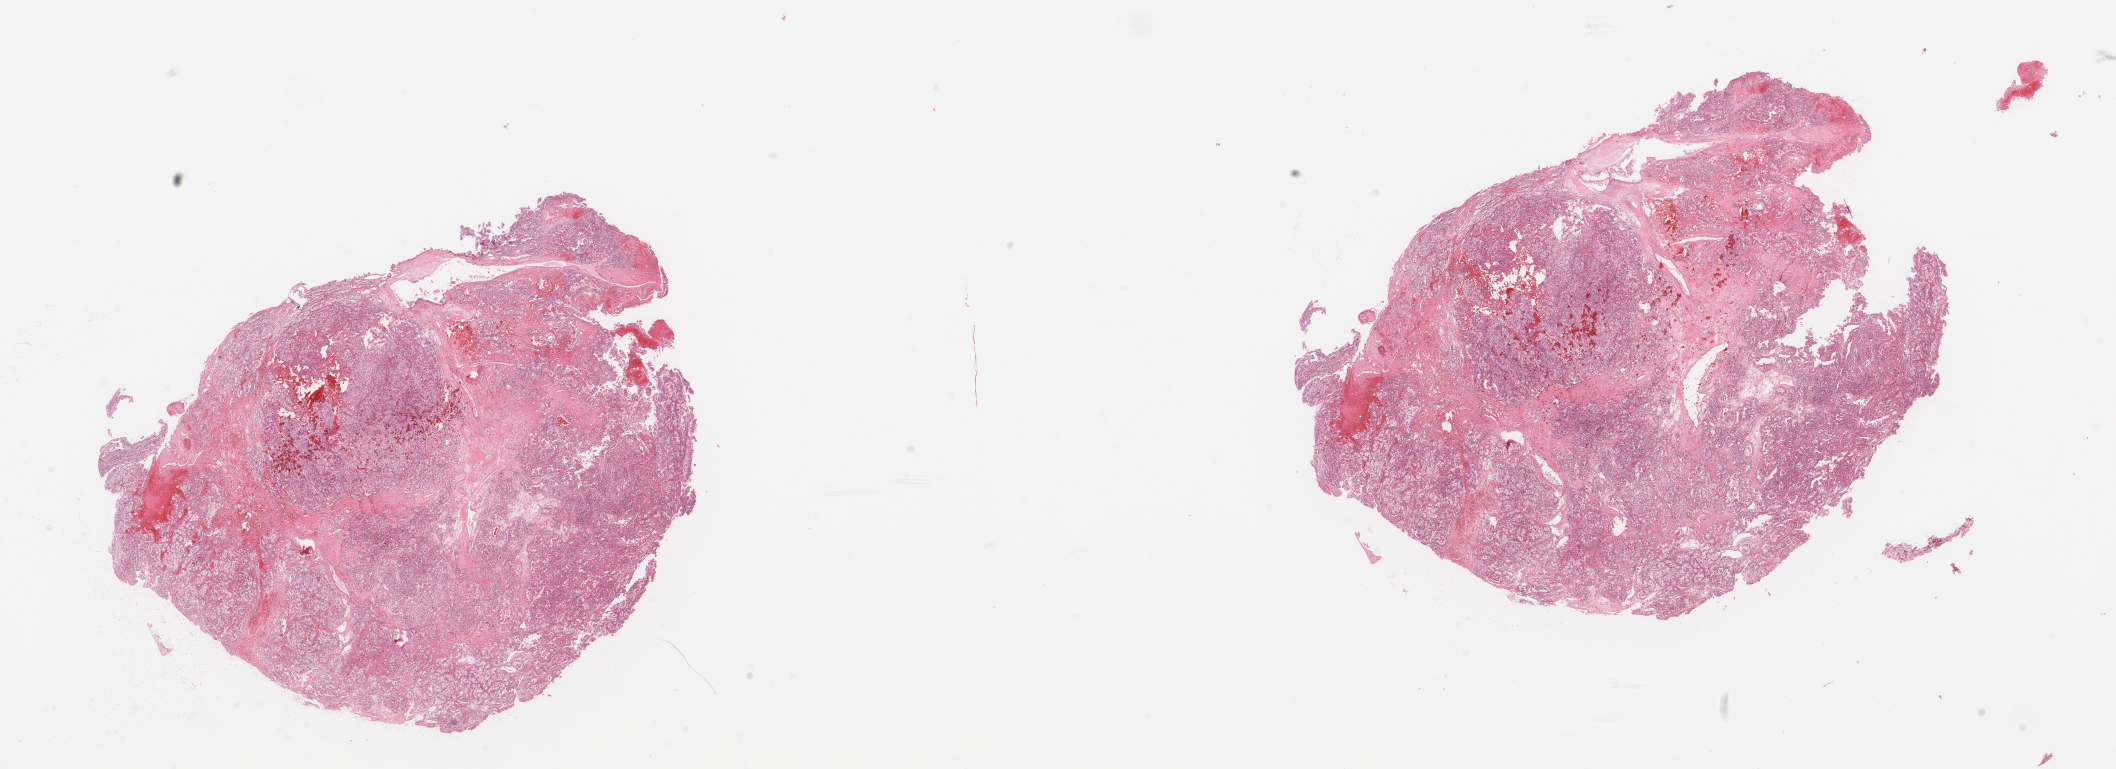
Hematoxylin and eosin (H&E) stained whole-slide image — whole scanned area (about 33.5 x 12.2 mm, slide scanned at 20x) shown as a low-resolution overview; kidney, tumour tissue. Male, 74 y/o. Histologic grade: G3 (poorly differentiated).
* primary tumour site (as recorded): lower pole
* AJCC pathologic stage: I
* histologic diagnosis: Renal cell carcinoma, NOS